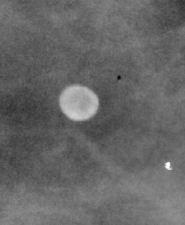
Crop from a digitized film mammogram around one marked abnormality, right breast, MLO view.
Marked abnormality: calcifications, morphology lucent center; BI-RADS assessment category 2; subtlety rating 5 on a 1 (subtle) to 5 (obvious) scale; benign without callback (not worked up further).